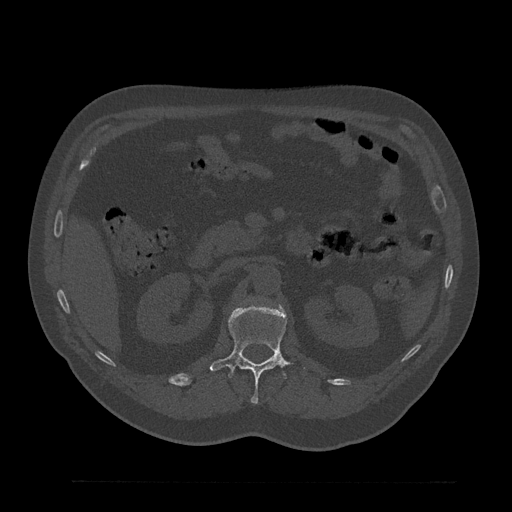
CT including the spine, one axial slice. Position 162 of 797 along the scan axis. Reconstruction kernel Br40s/3. 120 kVp. Bone window (W 1800 / L 400 HU). 512 × 512 image matrix. Male patient, age 61 years. From the clinical record (not read from this slice): primary cancer: prostate.
Outlined on this slice (semi-automatic segmentation, software-assisted and operator-edited):
- L1 vertebra: box from (x=210, y=304) to (x=304, y=404) px